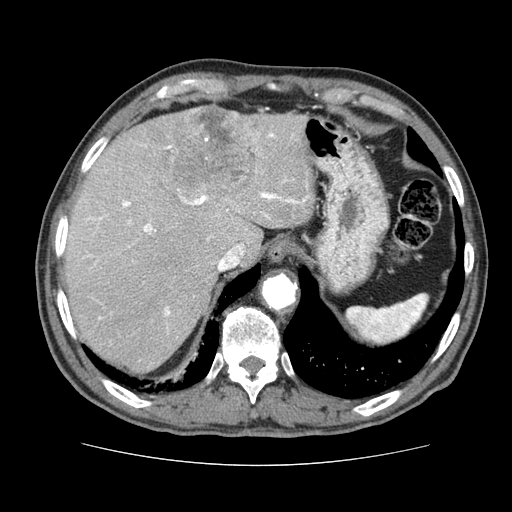
Contrast-enhanced abdominal CT (liver protocol), one axial slice; slice 58 of 79 in the series (ordered by position); reconstruction kernel STANDARD; 120 kVp; soft-tissue window (W 400 / L 40 HU); 512 × 512 image matrix. From the clinical record (not read from this slice): diagnosis: hepatocellular carcinoma (patient treated with transarterial chemoembolisation; whether this scan precedes or follows treatment is not stated here); TNM stage (as recorded): Stage-I; Child-Pugh class: A; tumour nodularity: uninodular.
Annotated regions visible in this slice (semi-automatic segmentation, software-assisted and operator-edited):
- liver parenchyma outside the tumour (the mass and vessels are separate outlines, so this box may not span the whole liver): bounding box (x1, y1, x2, y2) in pixels: (64, 110, 314, 372)
- mass: (146, 104, 260, 205)
- liver vessels: (86, 133, 308, 319)